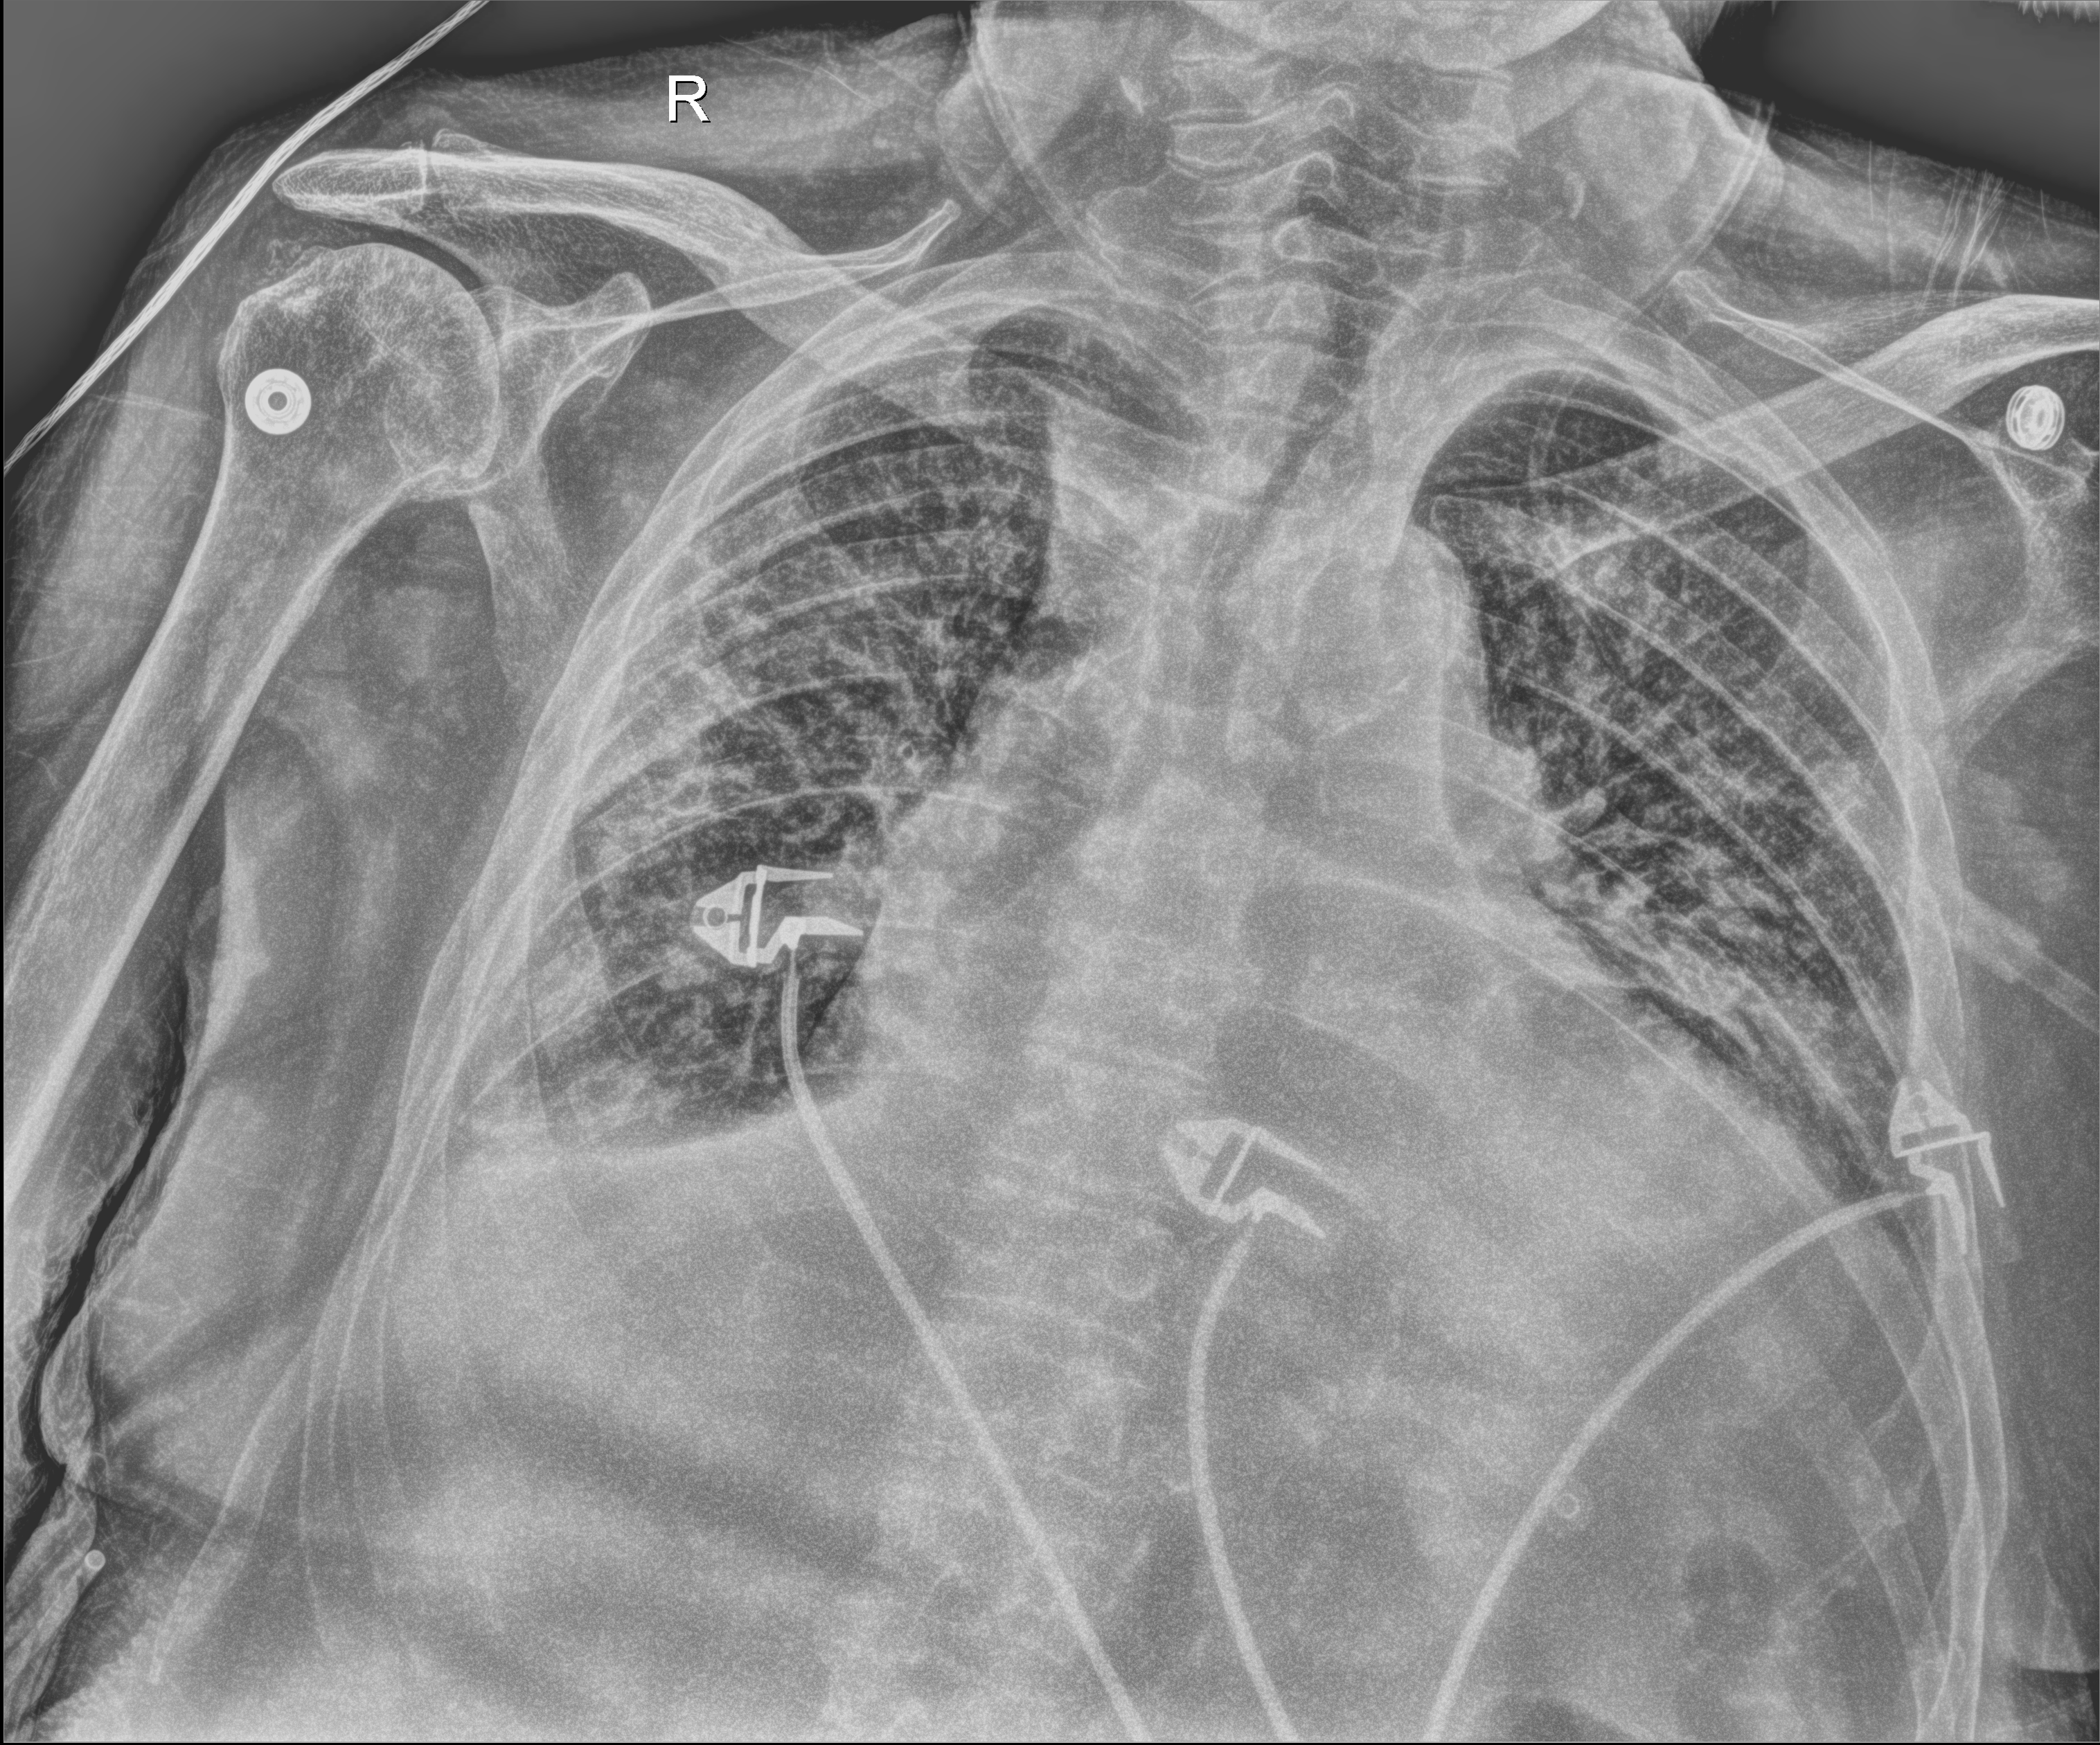
Bedside chest radiograph (digital radiography), anteroposterior (AP) projection. Patient hospitalised with COVID-19; male, aged 75–90 years.
Hospital-stay facts (about this admission, not read from this image; timing relative to this image not recorded): length of hospital stay: 20 days; mechanically ventilated during this hospital stay: no; smoking status (admission record): former.